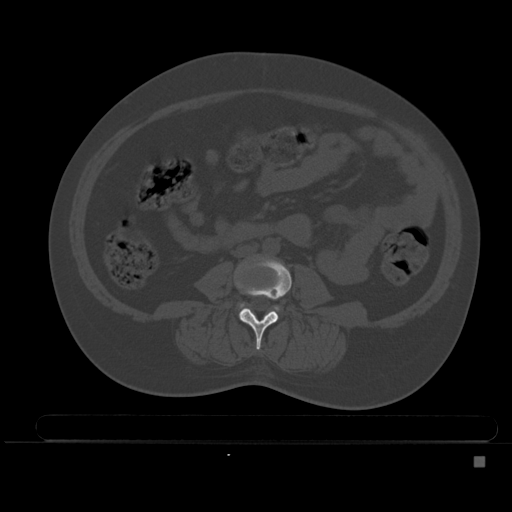
CT including the spine, one axial slice. Slice 144 of 495 in the series (ordered by position). Bone window (W 1800 / L 400 HU). 1.5 mm slice thickness. 512 × 512 image matrix, field of view 404 × 404 mm. Female patient, age 33 years. From the clinical record (not read from this slice): primary cancer: breast; vertebrae with lytic lesions (as recorded): T1.
Structures marked on this image (semi-automatic segmentation, software-assisted and operator-edited):
- L3 vertebra: bounding box <235,257,292,350> (left, top, right, bottom; pixels)